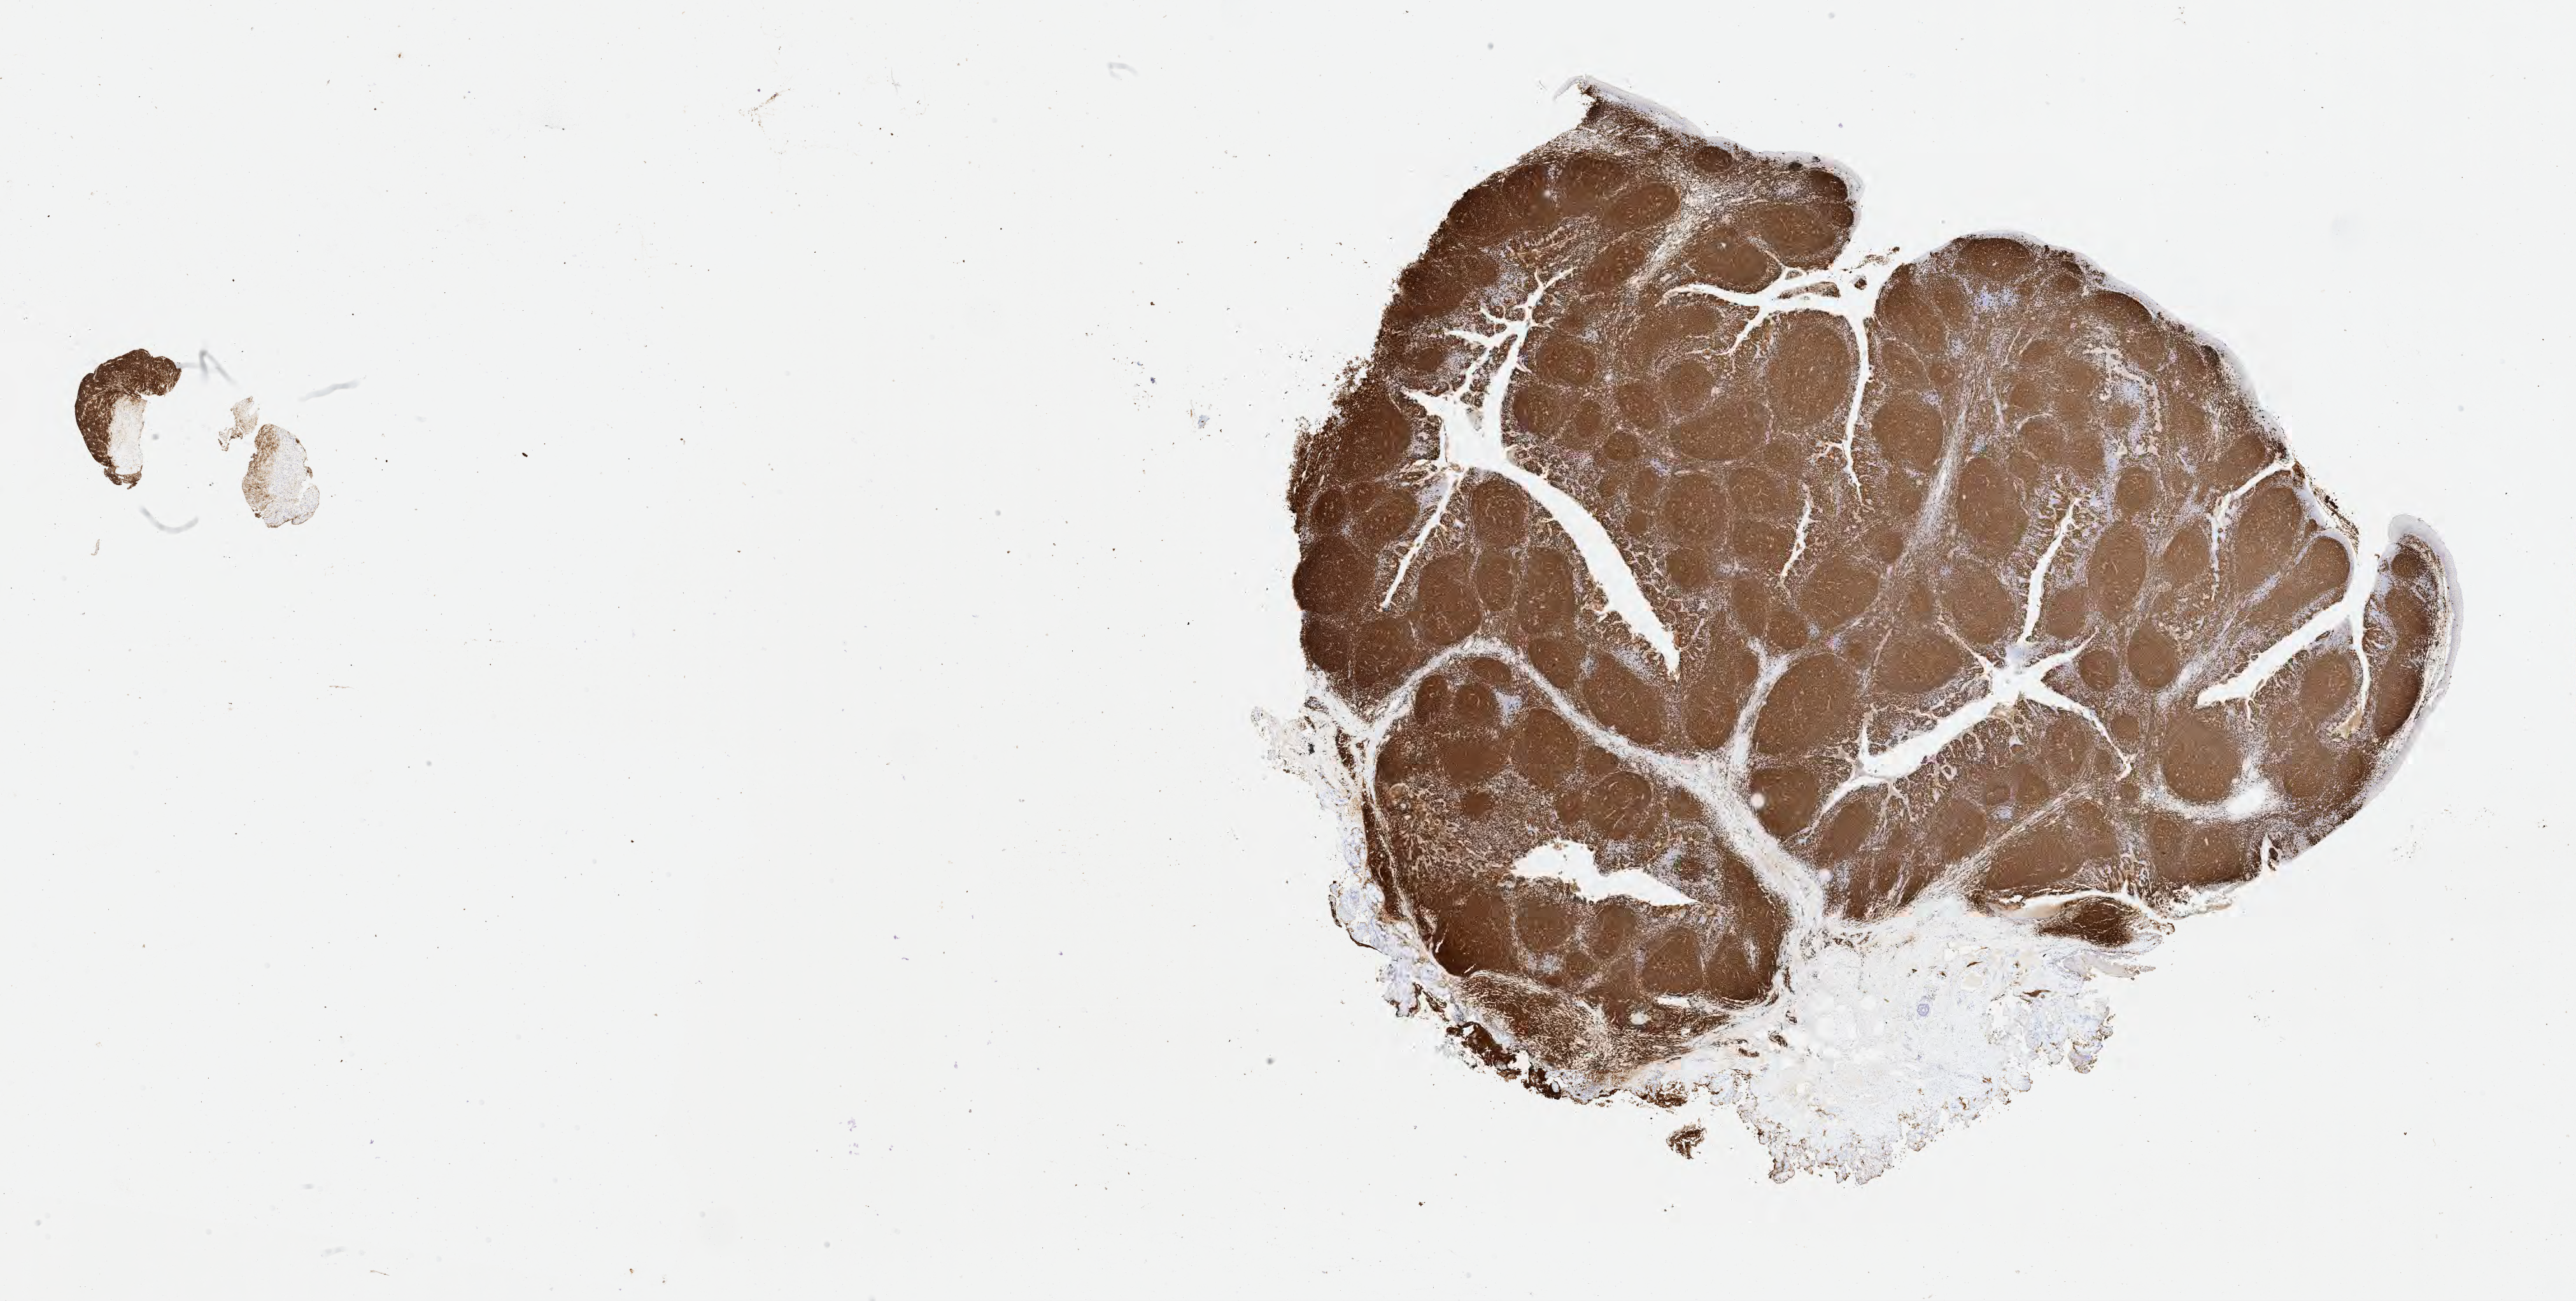
IHC for CD20, whole-slide image, low-resolution overview of the scanned area, about 32.7 x 16.5 mm, specimen: tumor tissue, site: abdomen proper. Female, age 6 years at initial diagnosis.
Diagnosis: Diffuse large B-cell lymphoma, NOS.